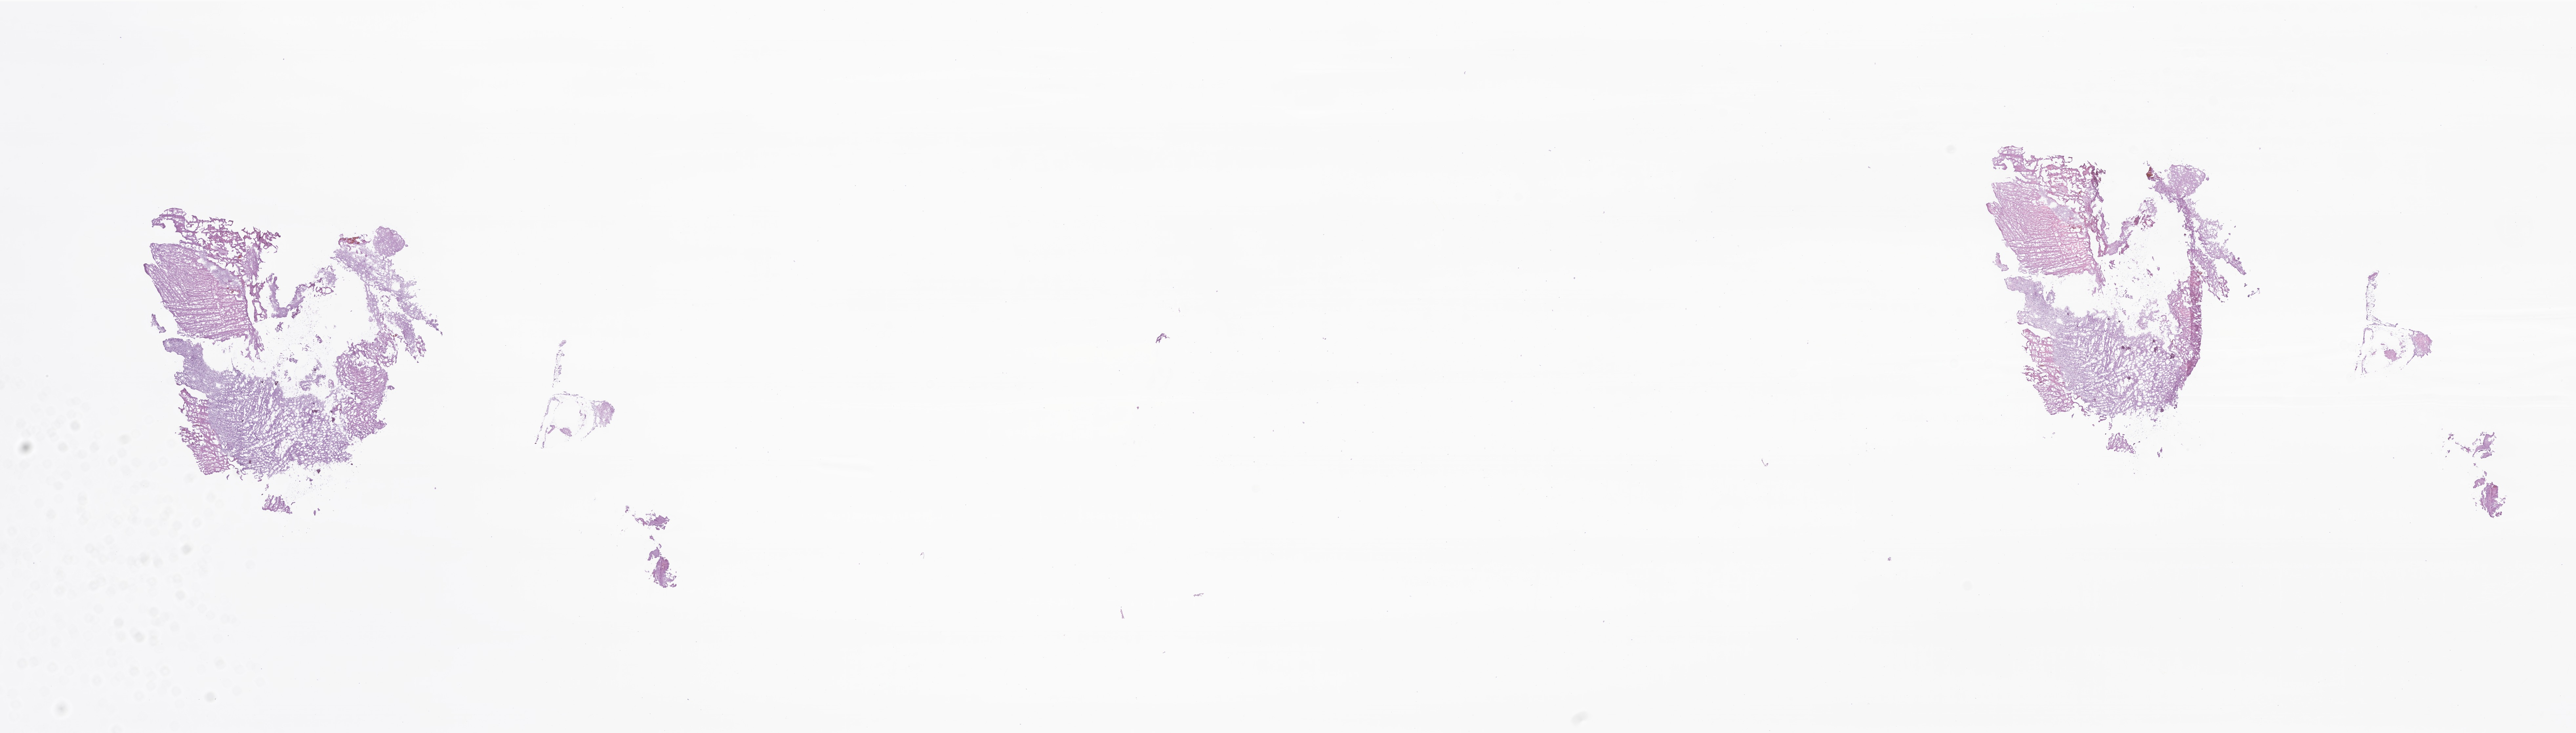
Whole-slide image, H&E stain of tumor tissue from the brain — low-resolution overview of the scanned area, about 33.1 x 9.4 mm, cryosection (OCT / tissue freezing medium). Patient: male, age 617 days (about 1.7 years).
- diagnosis (ICD-O-3 morphology term): Dysembryoplastic neuroepithelial tumor